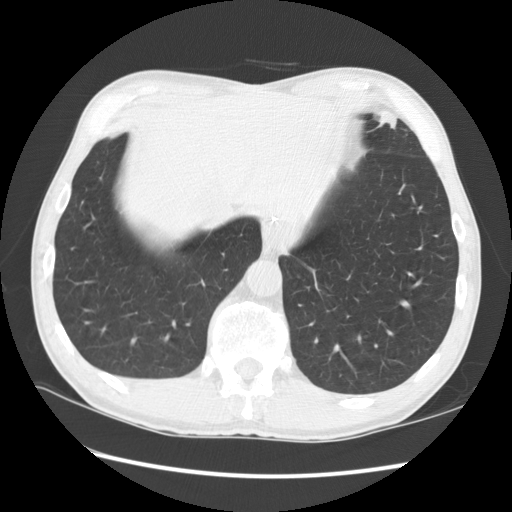
Low-dose screening chest CT, one axial slice; position 27 of 141 along the scan axis; lung window (W 1500 / L -600 HU); 512 × 512 image matrix, field of view 360 × 360 mm.
Outlined on this slice (expert manual segmentation):
- lesion 1 (tumor, lower lobe of left lung): bounding box (x1, y1, x2, y2) in pixels: (374, 113, 398, 129)